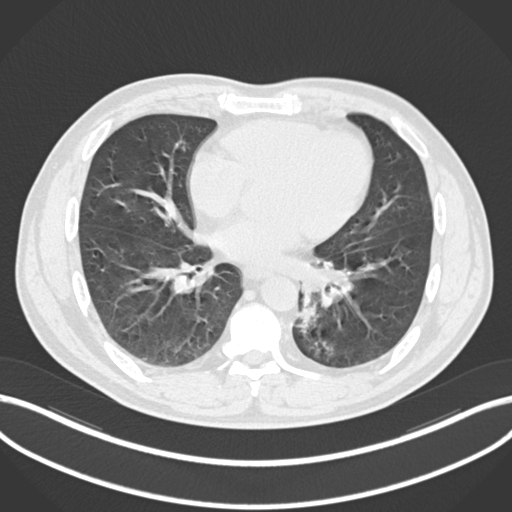
Chest CT, one axial slice; slice 92 of 223 in the series (ordered by position); 120 kVp; lung window (W 1500 / L -600 HU); 1 mm slice thickness; 512 × 512 image matrix, field of view 400 × 400 mm. Male patient, age 50 years. Case-level facts recorded for this patient, not image findings: clinical TNM (as recorded): T2a N3 M0.
Outlined on this slice (bounding box drawn by a radiologist):
- lung tumour (recorded histology: squamous cell carcinoma): bounding box [x1, y1, x2, y2] px = [297, 290, 322, 336]